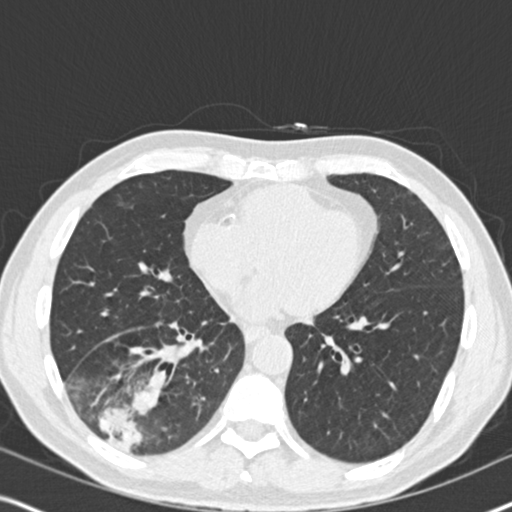
Axial slice from a low-dose chest CT screening exam, second screening round (one year after baseline), lung window (W 1500 / L -600 HU), 120 kVp, slice 103 of 182 in the series, 512 × 512 image matrix. Male, age 61 years at enrolment. Current smoker at enrolment.
Lesion marked by an expert reader, bounding box [x1, y1, x2, y2] px = [57, 336, 192, 466]. Reader record for this screening exam (exam-level; its link to the box is not recorded): non-calcified nodule or mass ≥4 mm, right lower lobe, 90 × 80 mm, soft tissue attenuation, pre-existing on the prior screen: yes; interval growth: yes. Official screen result: positive, other.